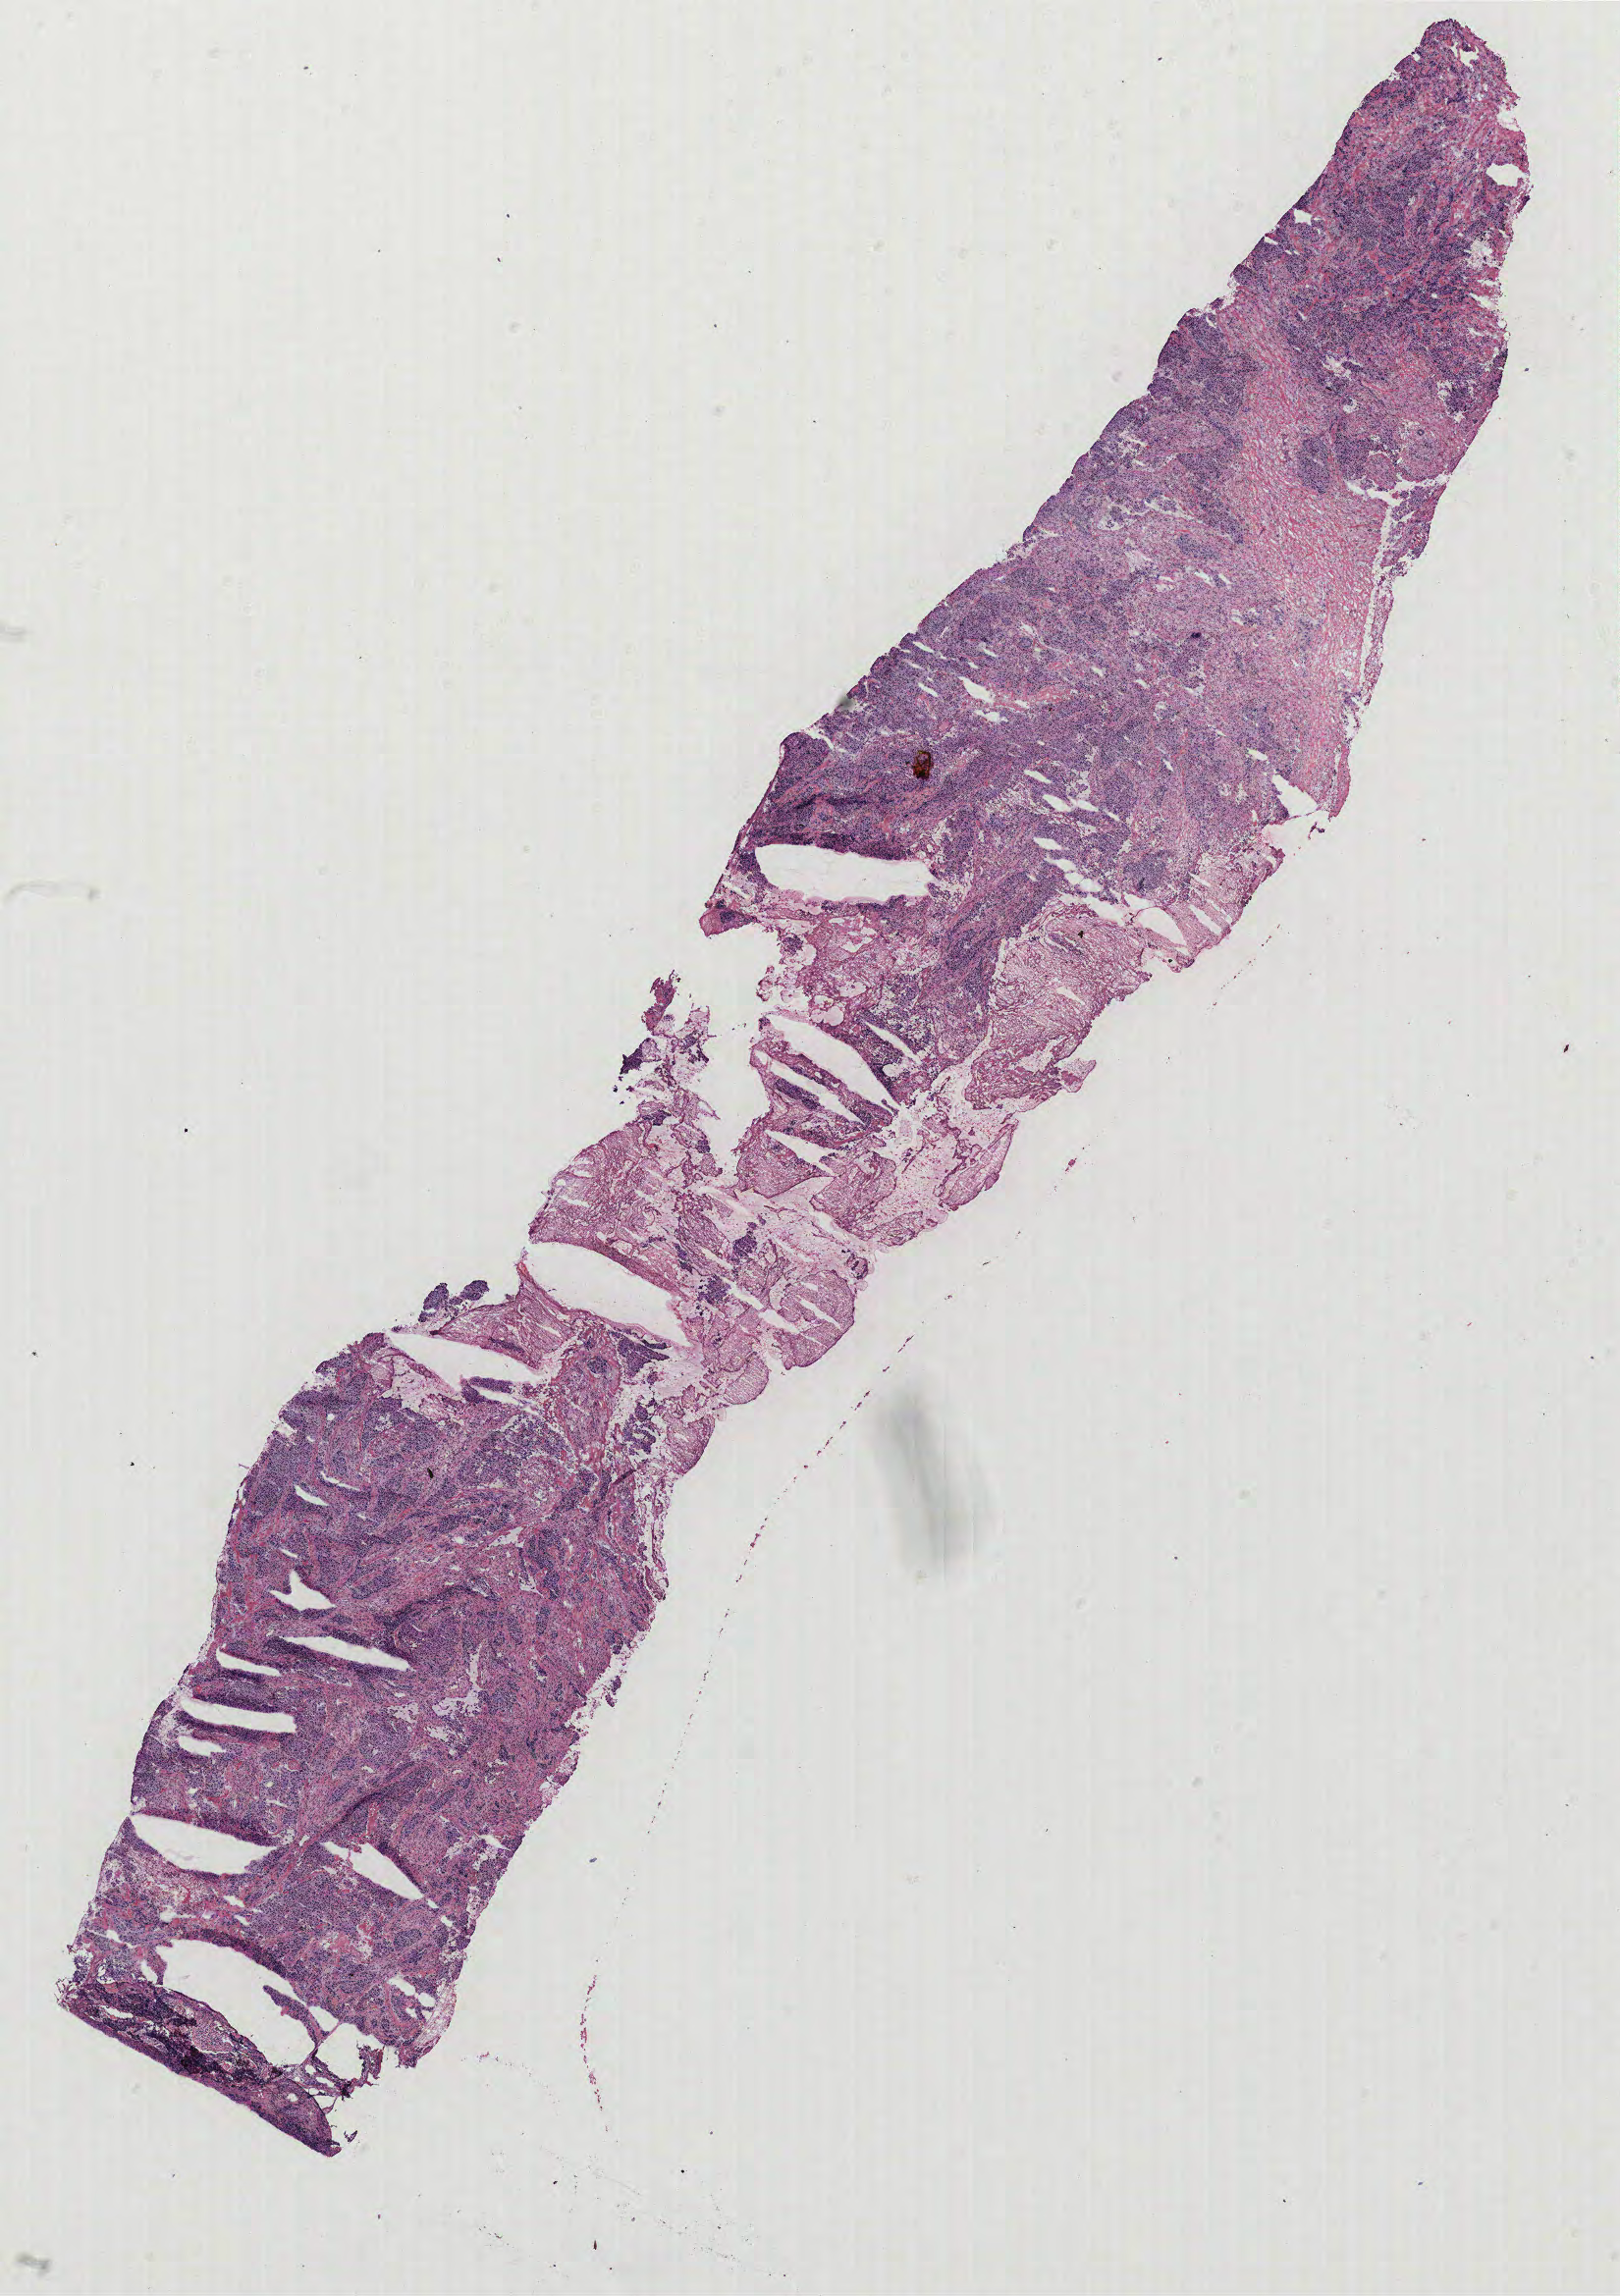
Hematoxylin and eosin (H&E) stained whole-slide image, shown as a low-resolution overview of the whole scanned area (about 13.2 x 18.7 mm); breast, tumour tissue. Female, 61 y/o.
• AJCC pathologic stage: III
• histologic diagnosis: Infiltrating duct carcinoma, NOS